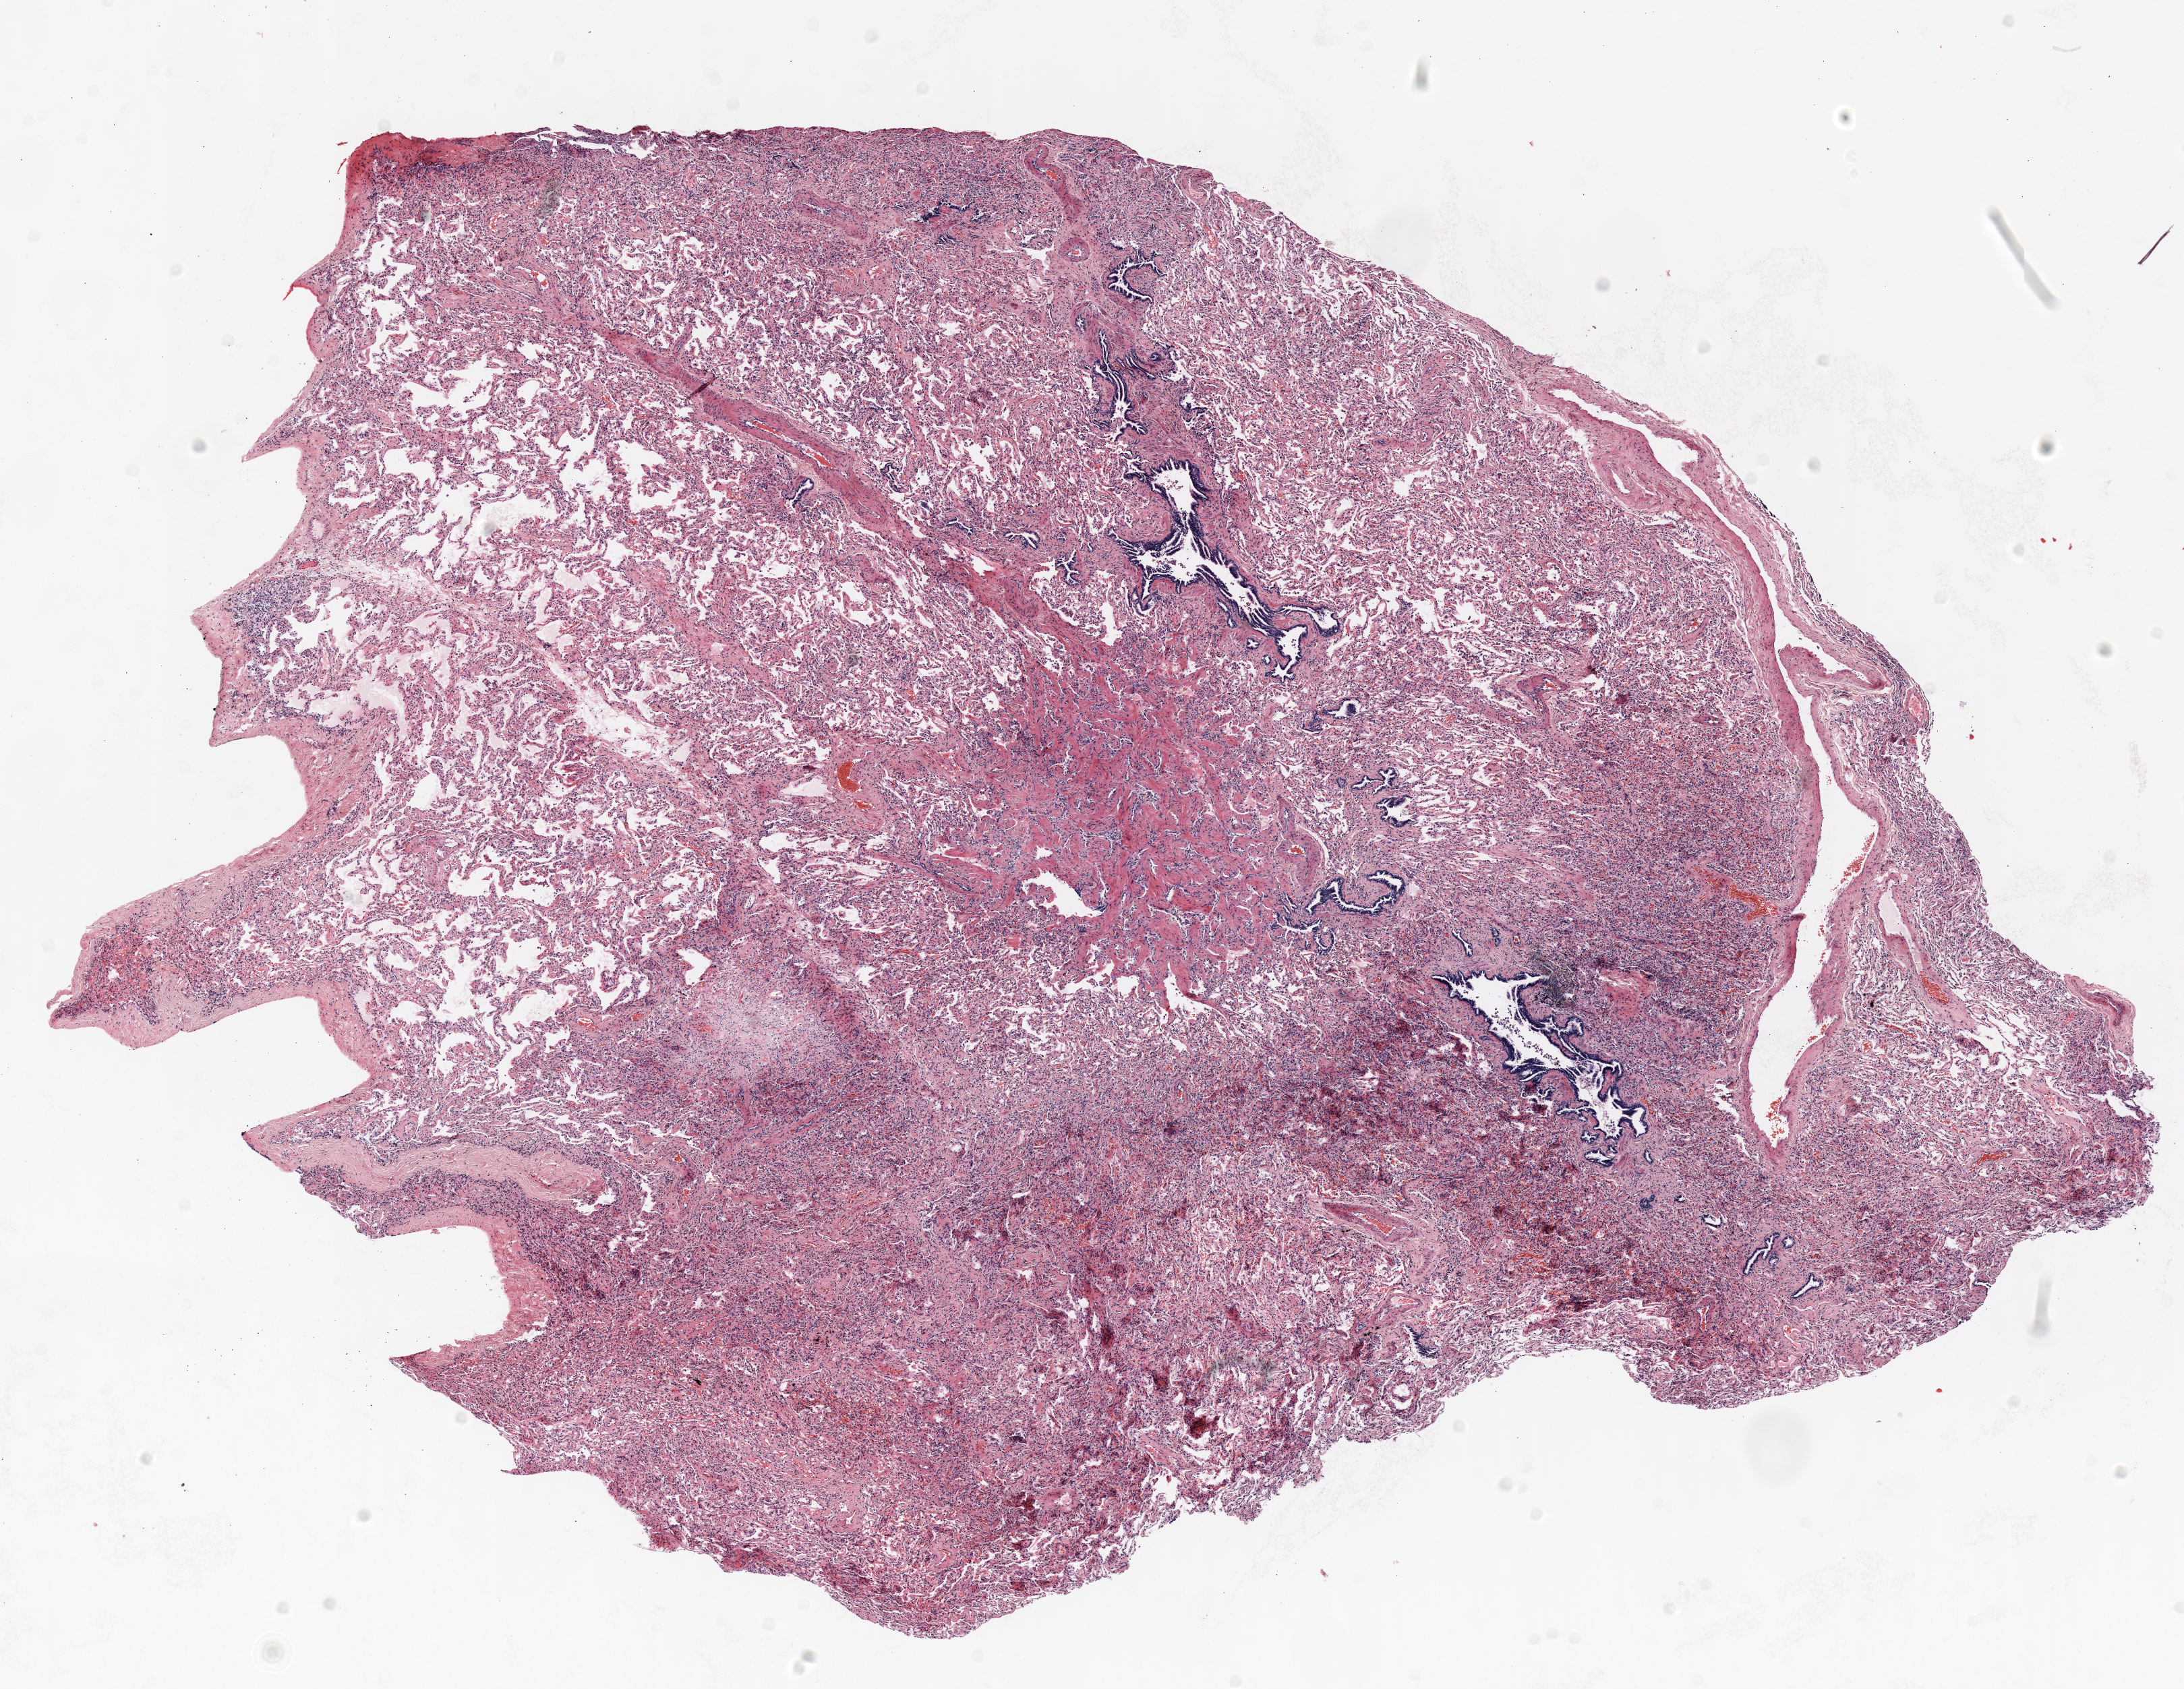
Whole-slide histology image, H&E — low-resolution overview of the scanned area, about 13.0 x 10.1 mm (acquisition: 20x scan). Formalin-fixed paraffin-embedded (FFPE) section. Lung. Female, age 59 at enrolment. Grade: well differentiated (G1).
Participant's lung-cancer diagnosis: Bronchiolo-alveolar adenocarcinoma, NOS. Primary tumour location (clinical record): left upper lobe. Tumour size (pathology): 10 mm. ICD-O-3 topography: upper lobe of lung (C34.1). Stage (AJCC 6th edition): IA.